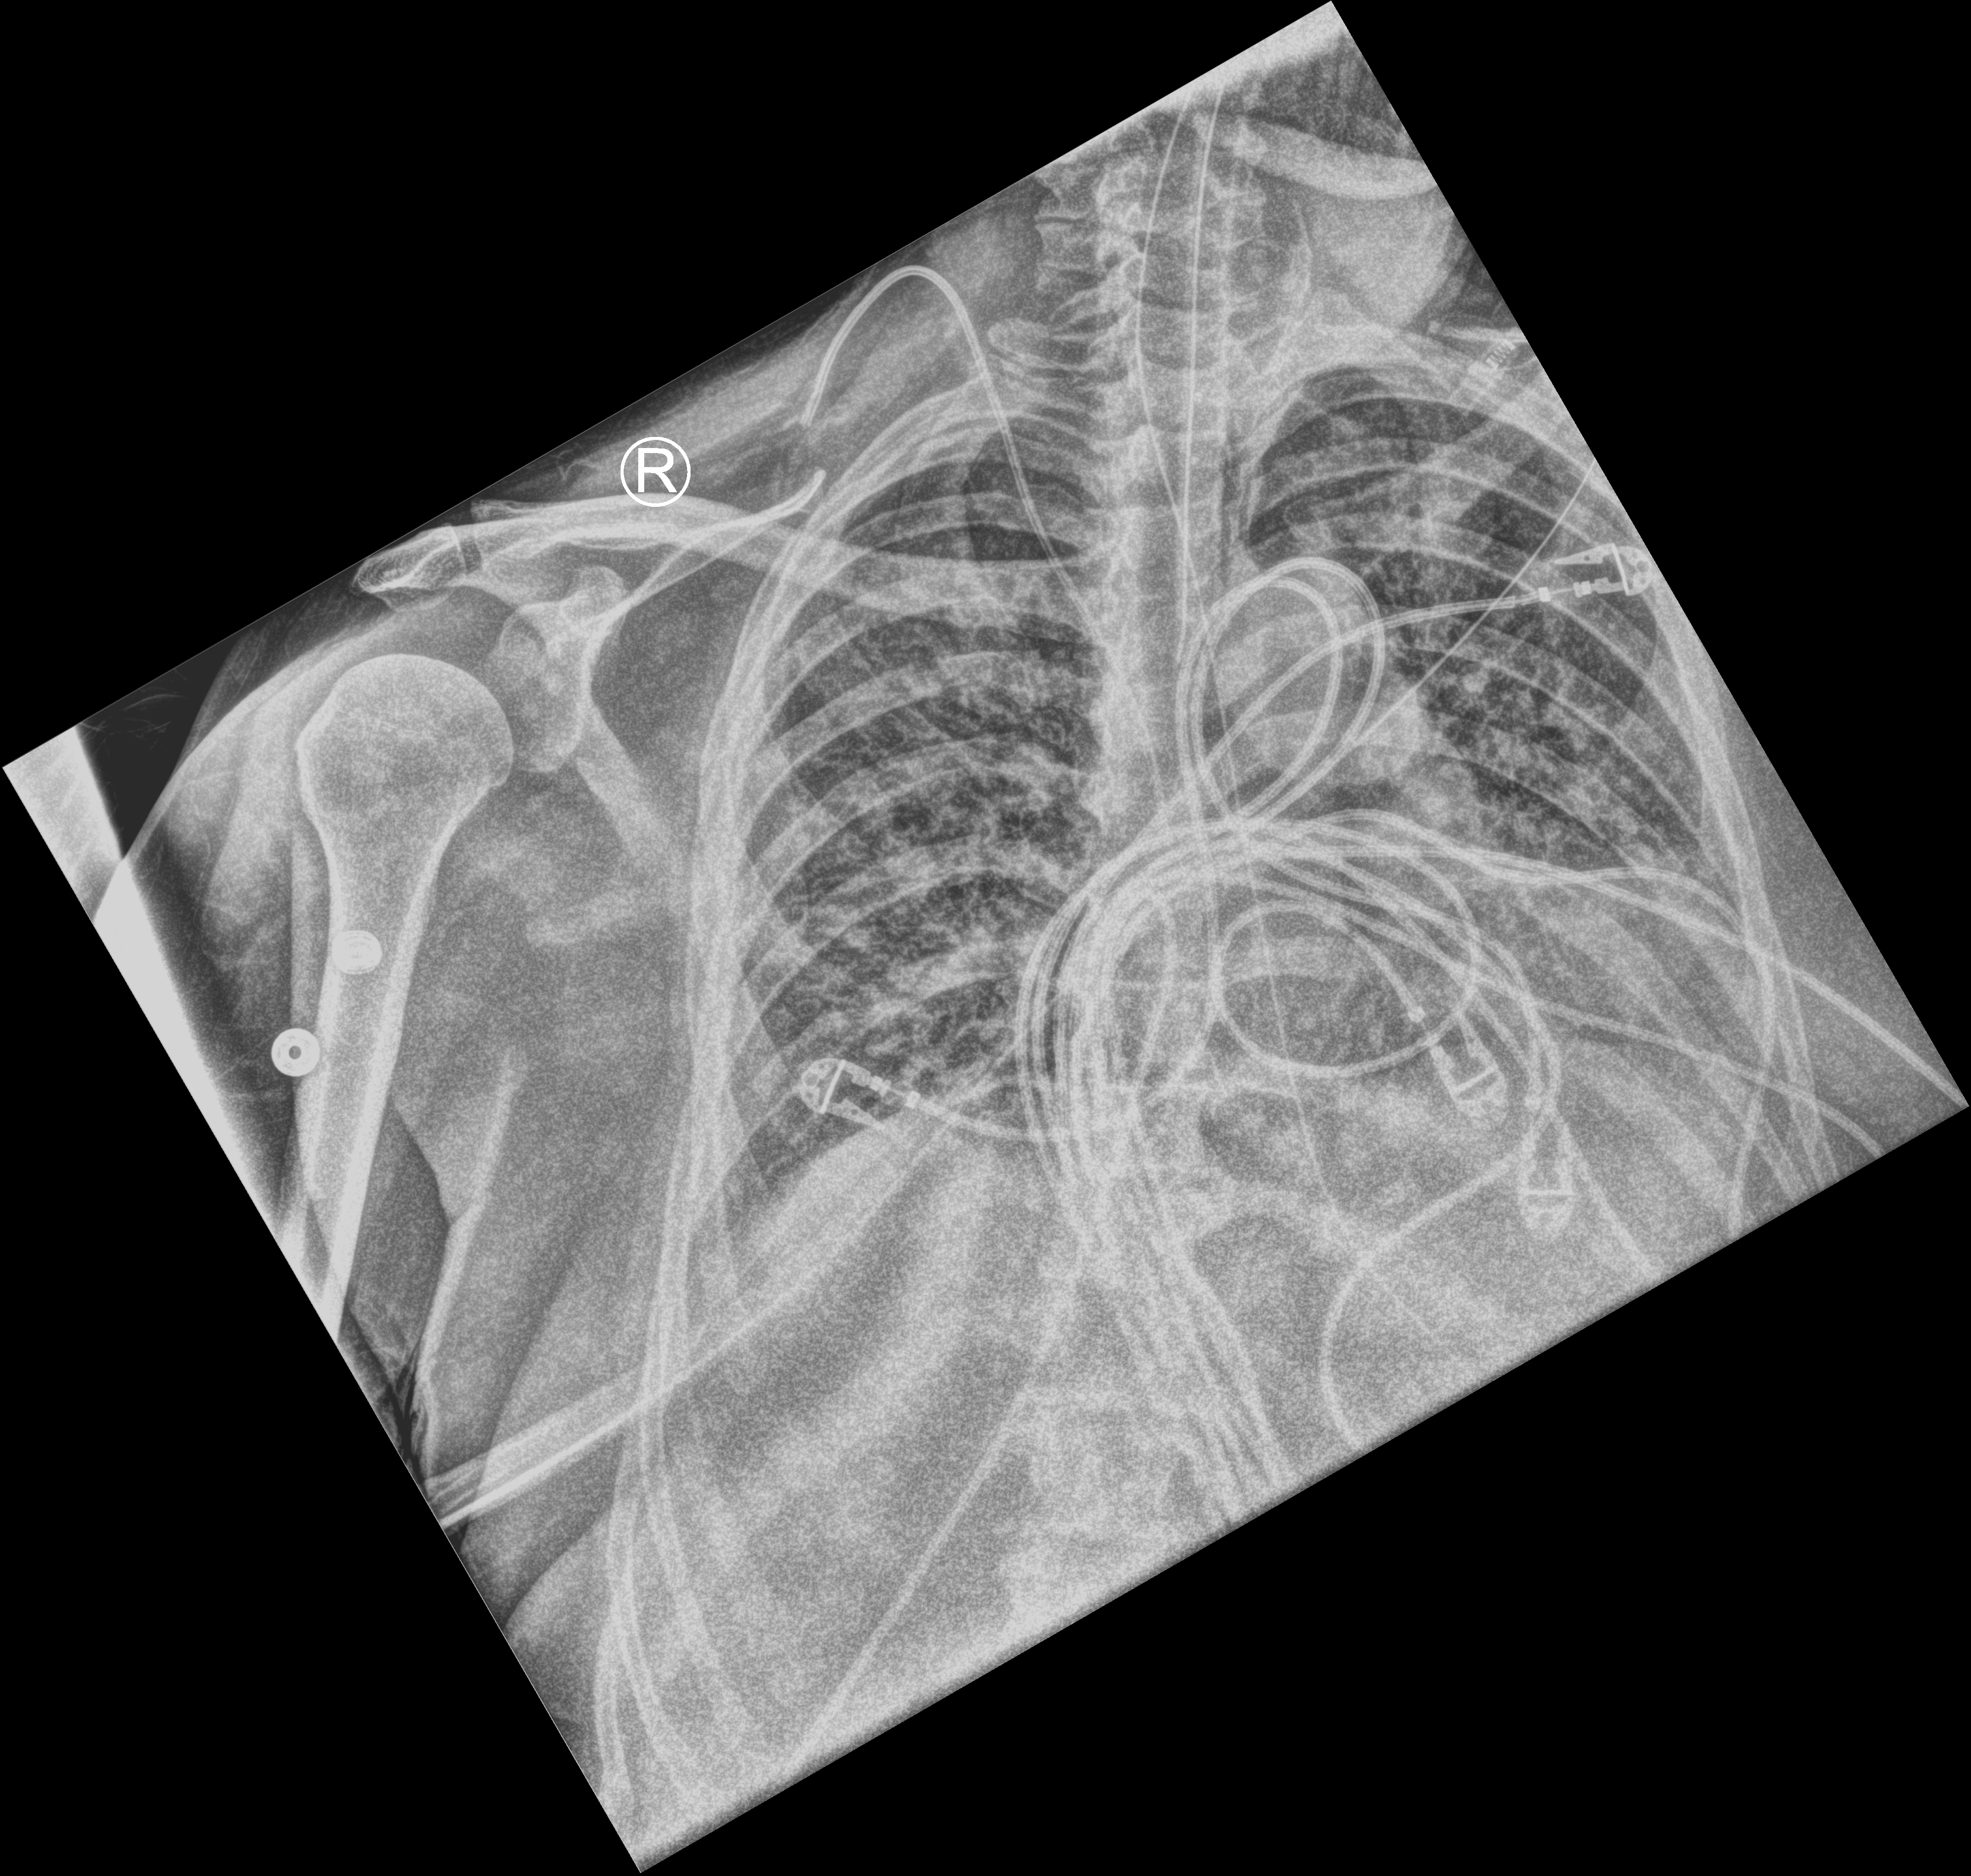
Chest X-ray (portable), anteroposterior (AP) projection. Patient hospitalised with COVID-19; male, aged 60–74 years.
Admission-level facts for this patient (not findings on this image; timing relative to this image not recorded):
- diabetes (admission record): no
- admitted to intensive care during this hospital stay: yes
- mechanically ventilated during this hospital stay: yes